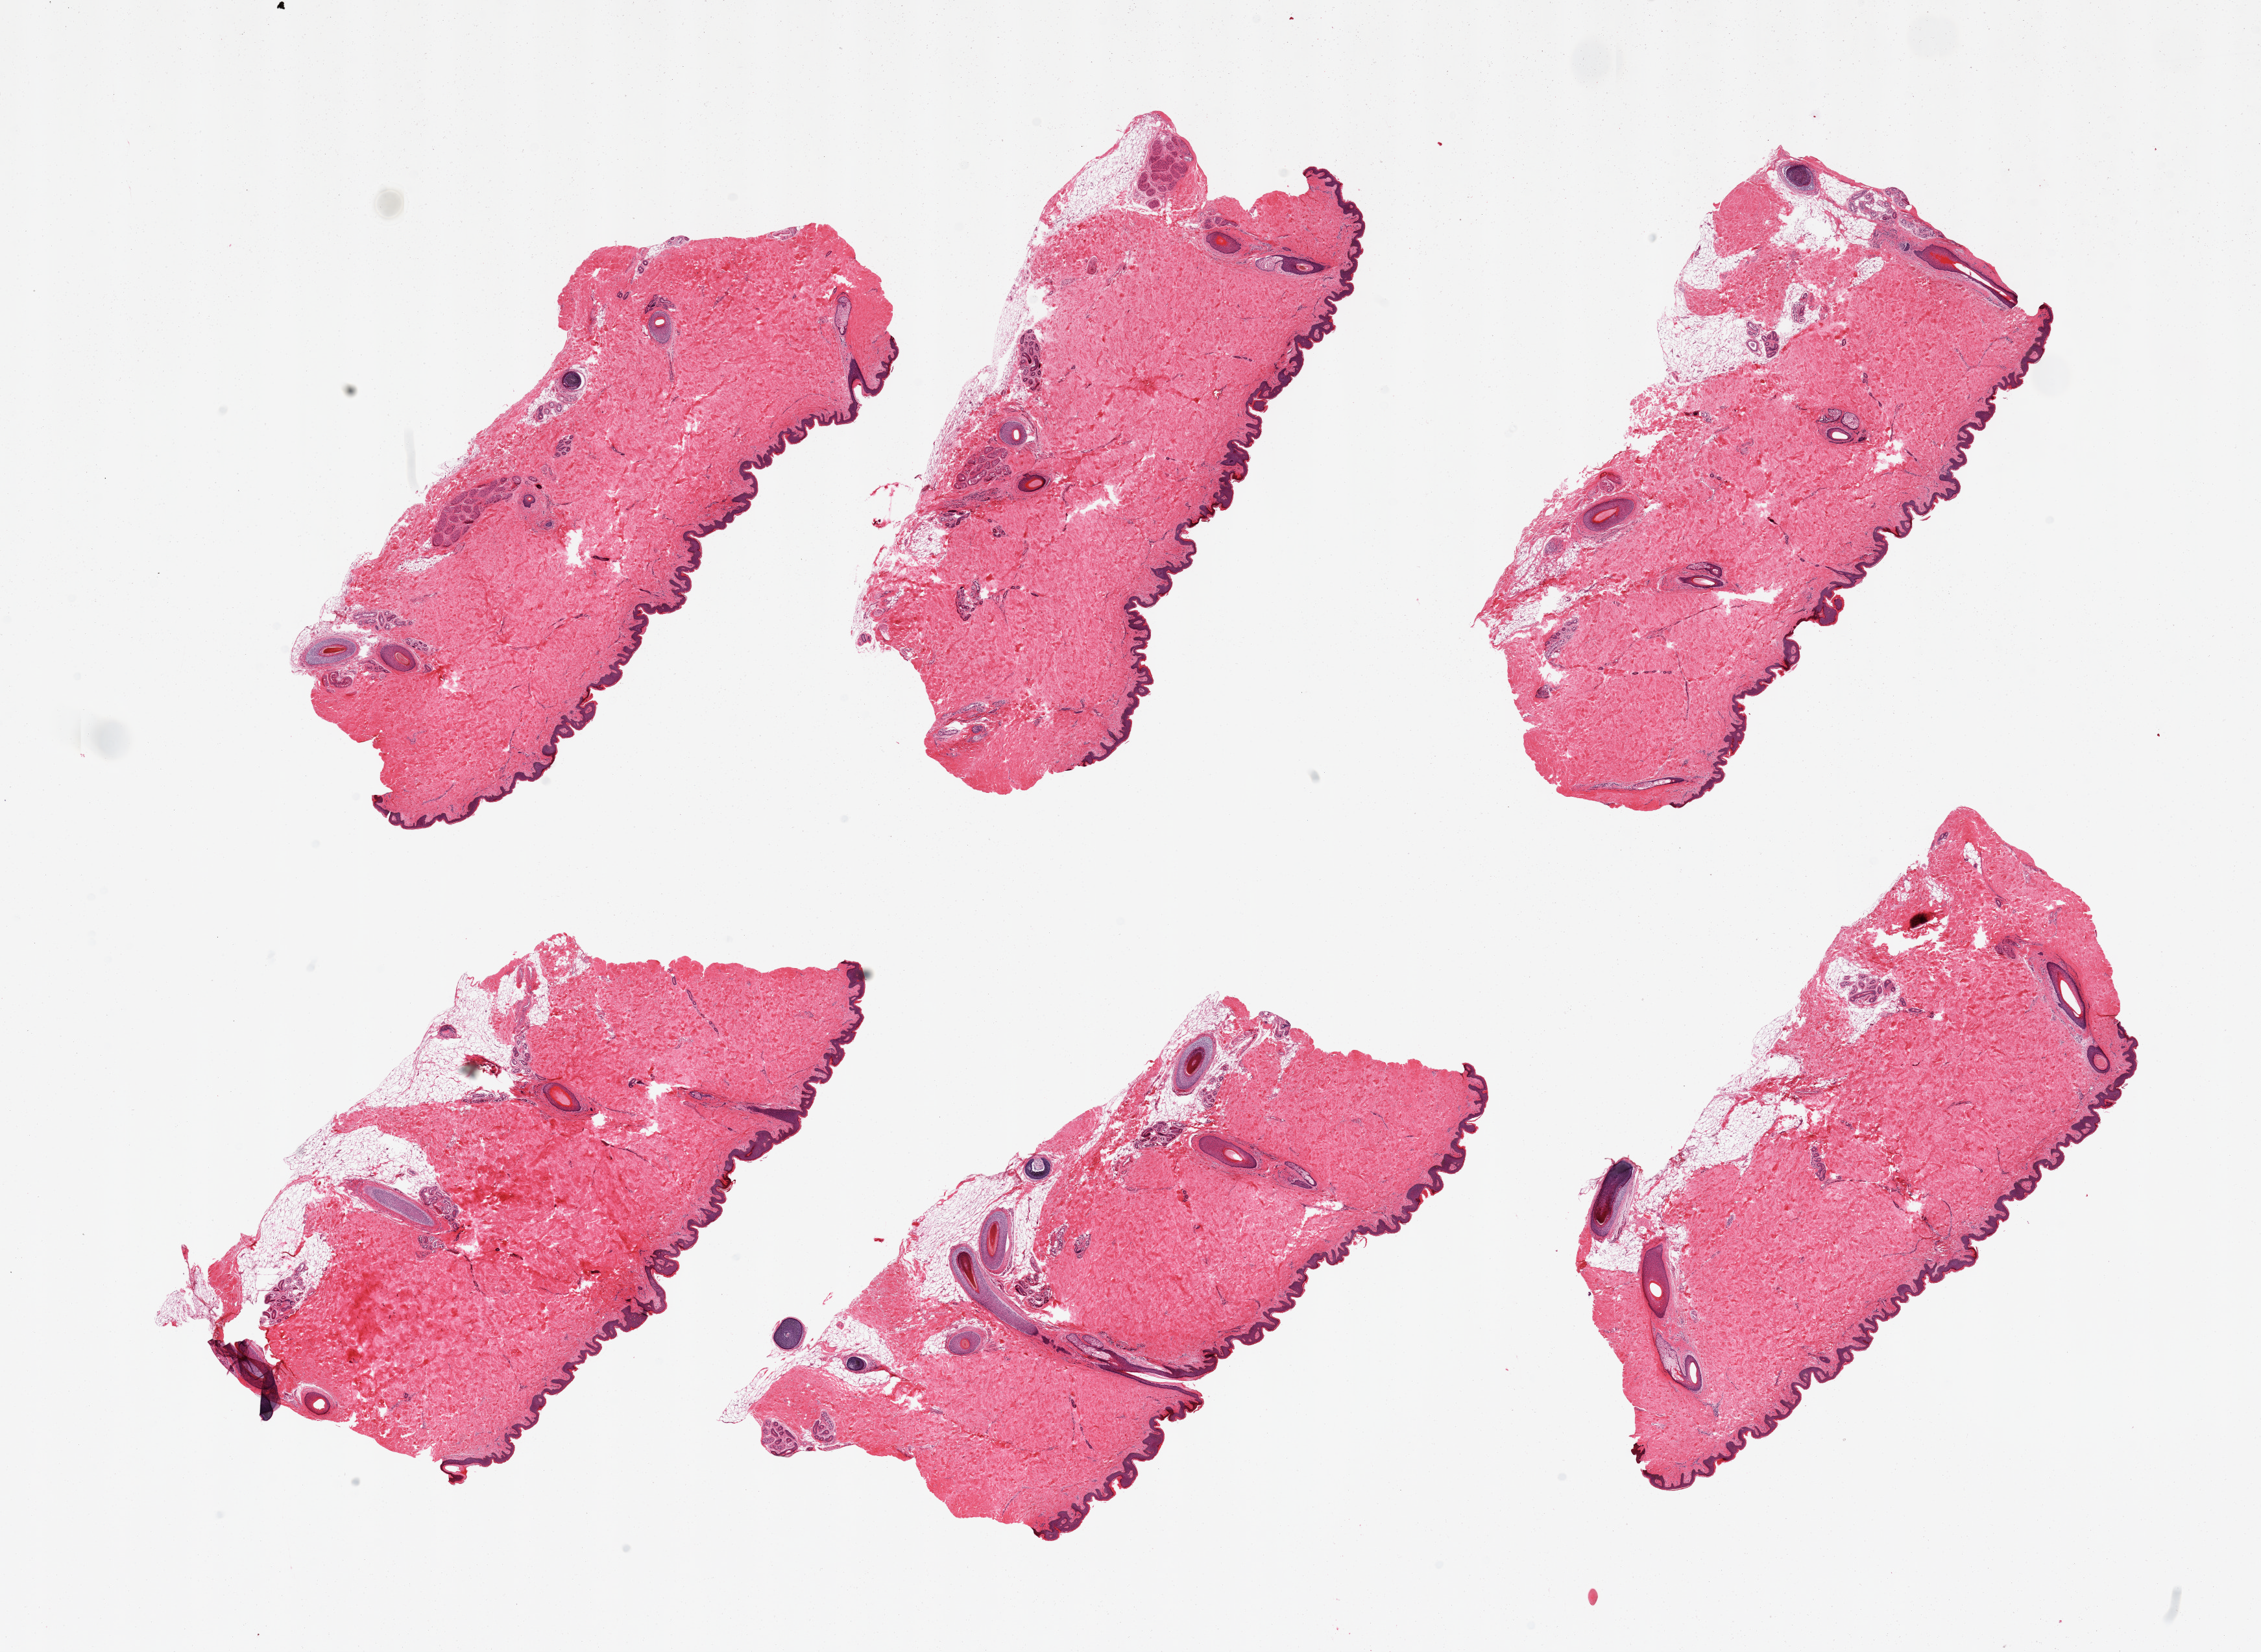
H&E whole-slide image, whole scanned area (about 27.6 x 20.1 mm, acquisition: 20x scan) shown as a low-resolution overview, PAXgene-fixed paraffin-embedded (PFPE) section, target tissue: skin of suprapubic region, donor tissue sample.
Pathologist's review note for this sample: 6 pieces. Hair-bearing. Well trimmed.